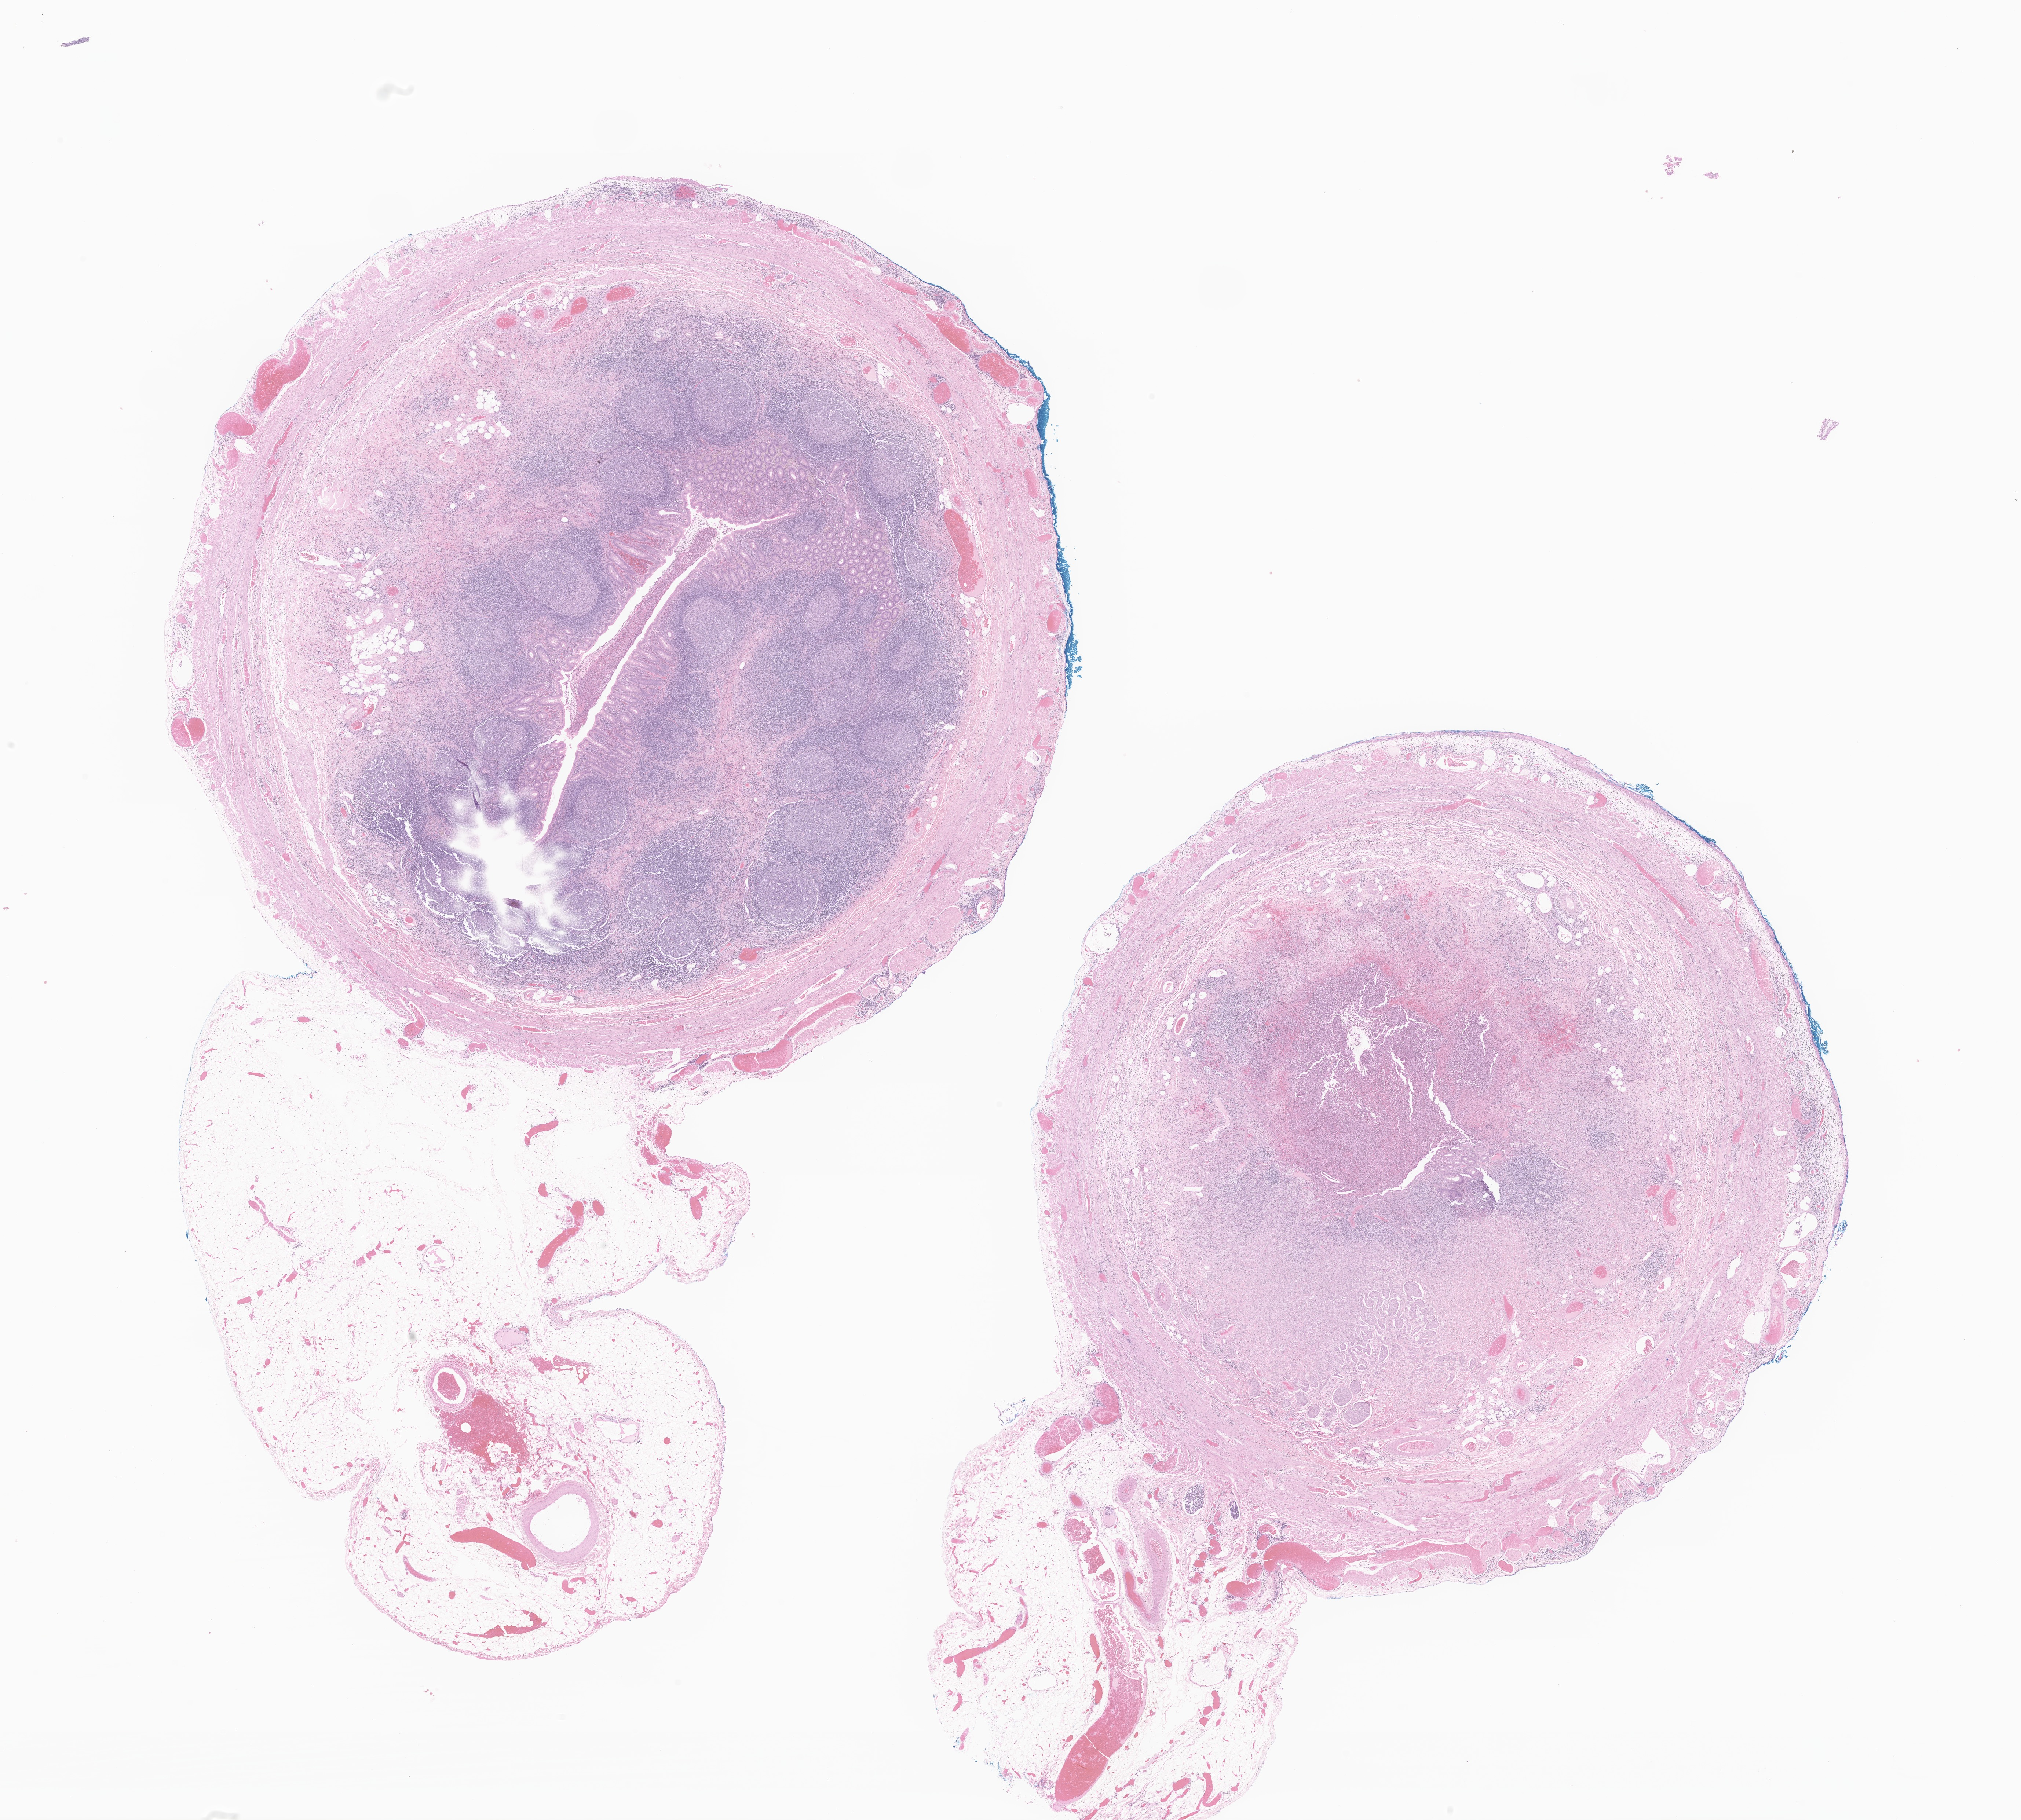
Haematoxylin and eosin whole-slide image of tumor tissue from the appendix, a low-resolution overview of the entire scanned area, about 23.2 x 20.9 mm. Formalin-fixed paraffin-embedded section. Patient: female, age 211 months.
Recorded diagnosis: Neuroendocrine carcinoma, NOS.